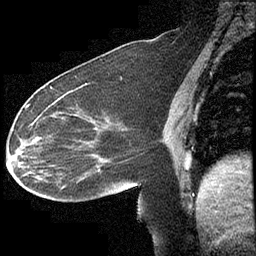
Breast MRI (dynamic contrast-enhanced), one sagittal slice; slice 161 of 232 in the series (ordered by position); dynamic contrast-enhanced study with each time point stored as its own series, time point 2 of 4 at this slice position (early post-contrast, ordered by acquisition time); 1.5 T; TE 4.2 ms, TR 6.7 ms; 3 mm slice thickness; 256 × 256 image matrix, field of view 200 × 200 mm. Patient: female, 63 years. Case-level facts recorded for this patient, not image findings: setting: breast cancer imaged before/during neoadjuvant chemotherapy; receptor status: triple-negative.
Outlined on this slice (semi-automatically segmented with operator editing):
- analysis volume of interest (the breast-tissue region the enhancement analysis was run in; not a lesion): bounding box <13,90,140,211> (left, top, right, bottom; pixels)
- tumour enhancement mask (voxels above the 70 % enhancement threshold inside the analysis volume of interest): <21,90,73,163>